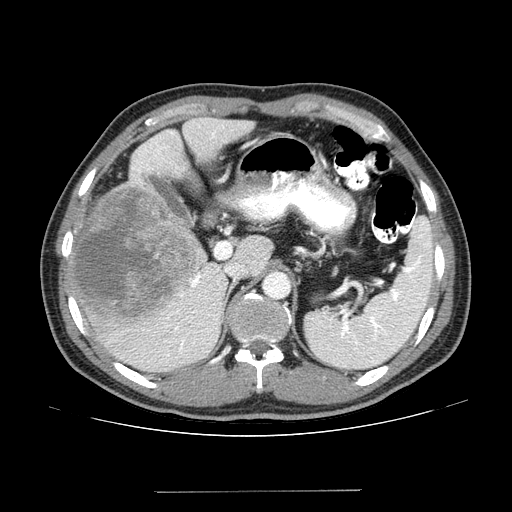
Contrast-enhanced abdominal CT (liver protocol), one axial slice. Slice 91 of 131 in the series (ordered by position). 100 kVp. One of 2 acquisitions stored at this slice position. Soft-tissue window (W 400 / L 40 HU). 2.5 mm slice thickness. 512 × 512 image matrix, field of view 380 × 380 mm. Case-level facts recorded for this patient, not image findings: diagnosis: hepatocellular carcinoma (patient treated with transarterial chemoembolisation; whether this scan precedes or follows treatment is not stated here); TNM stage (as recorded): Stage-I; Child-Pugh class: A; tumour size: 10.3 cm.
Outlined on this slice (semi-automatic segmentation, software-assisted and operator-edited):
- liver parenchyma outside the tumour (the mass and vessels are separate outlines, so this box may not span the whole liver): bounding box [x1, y1, x2, y2] px = [66, 116, 254, 372]
- mass: [67, 184, 205, 326]
- liver vessels: [132, 125, 224, 357]